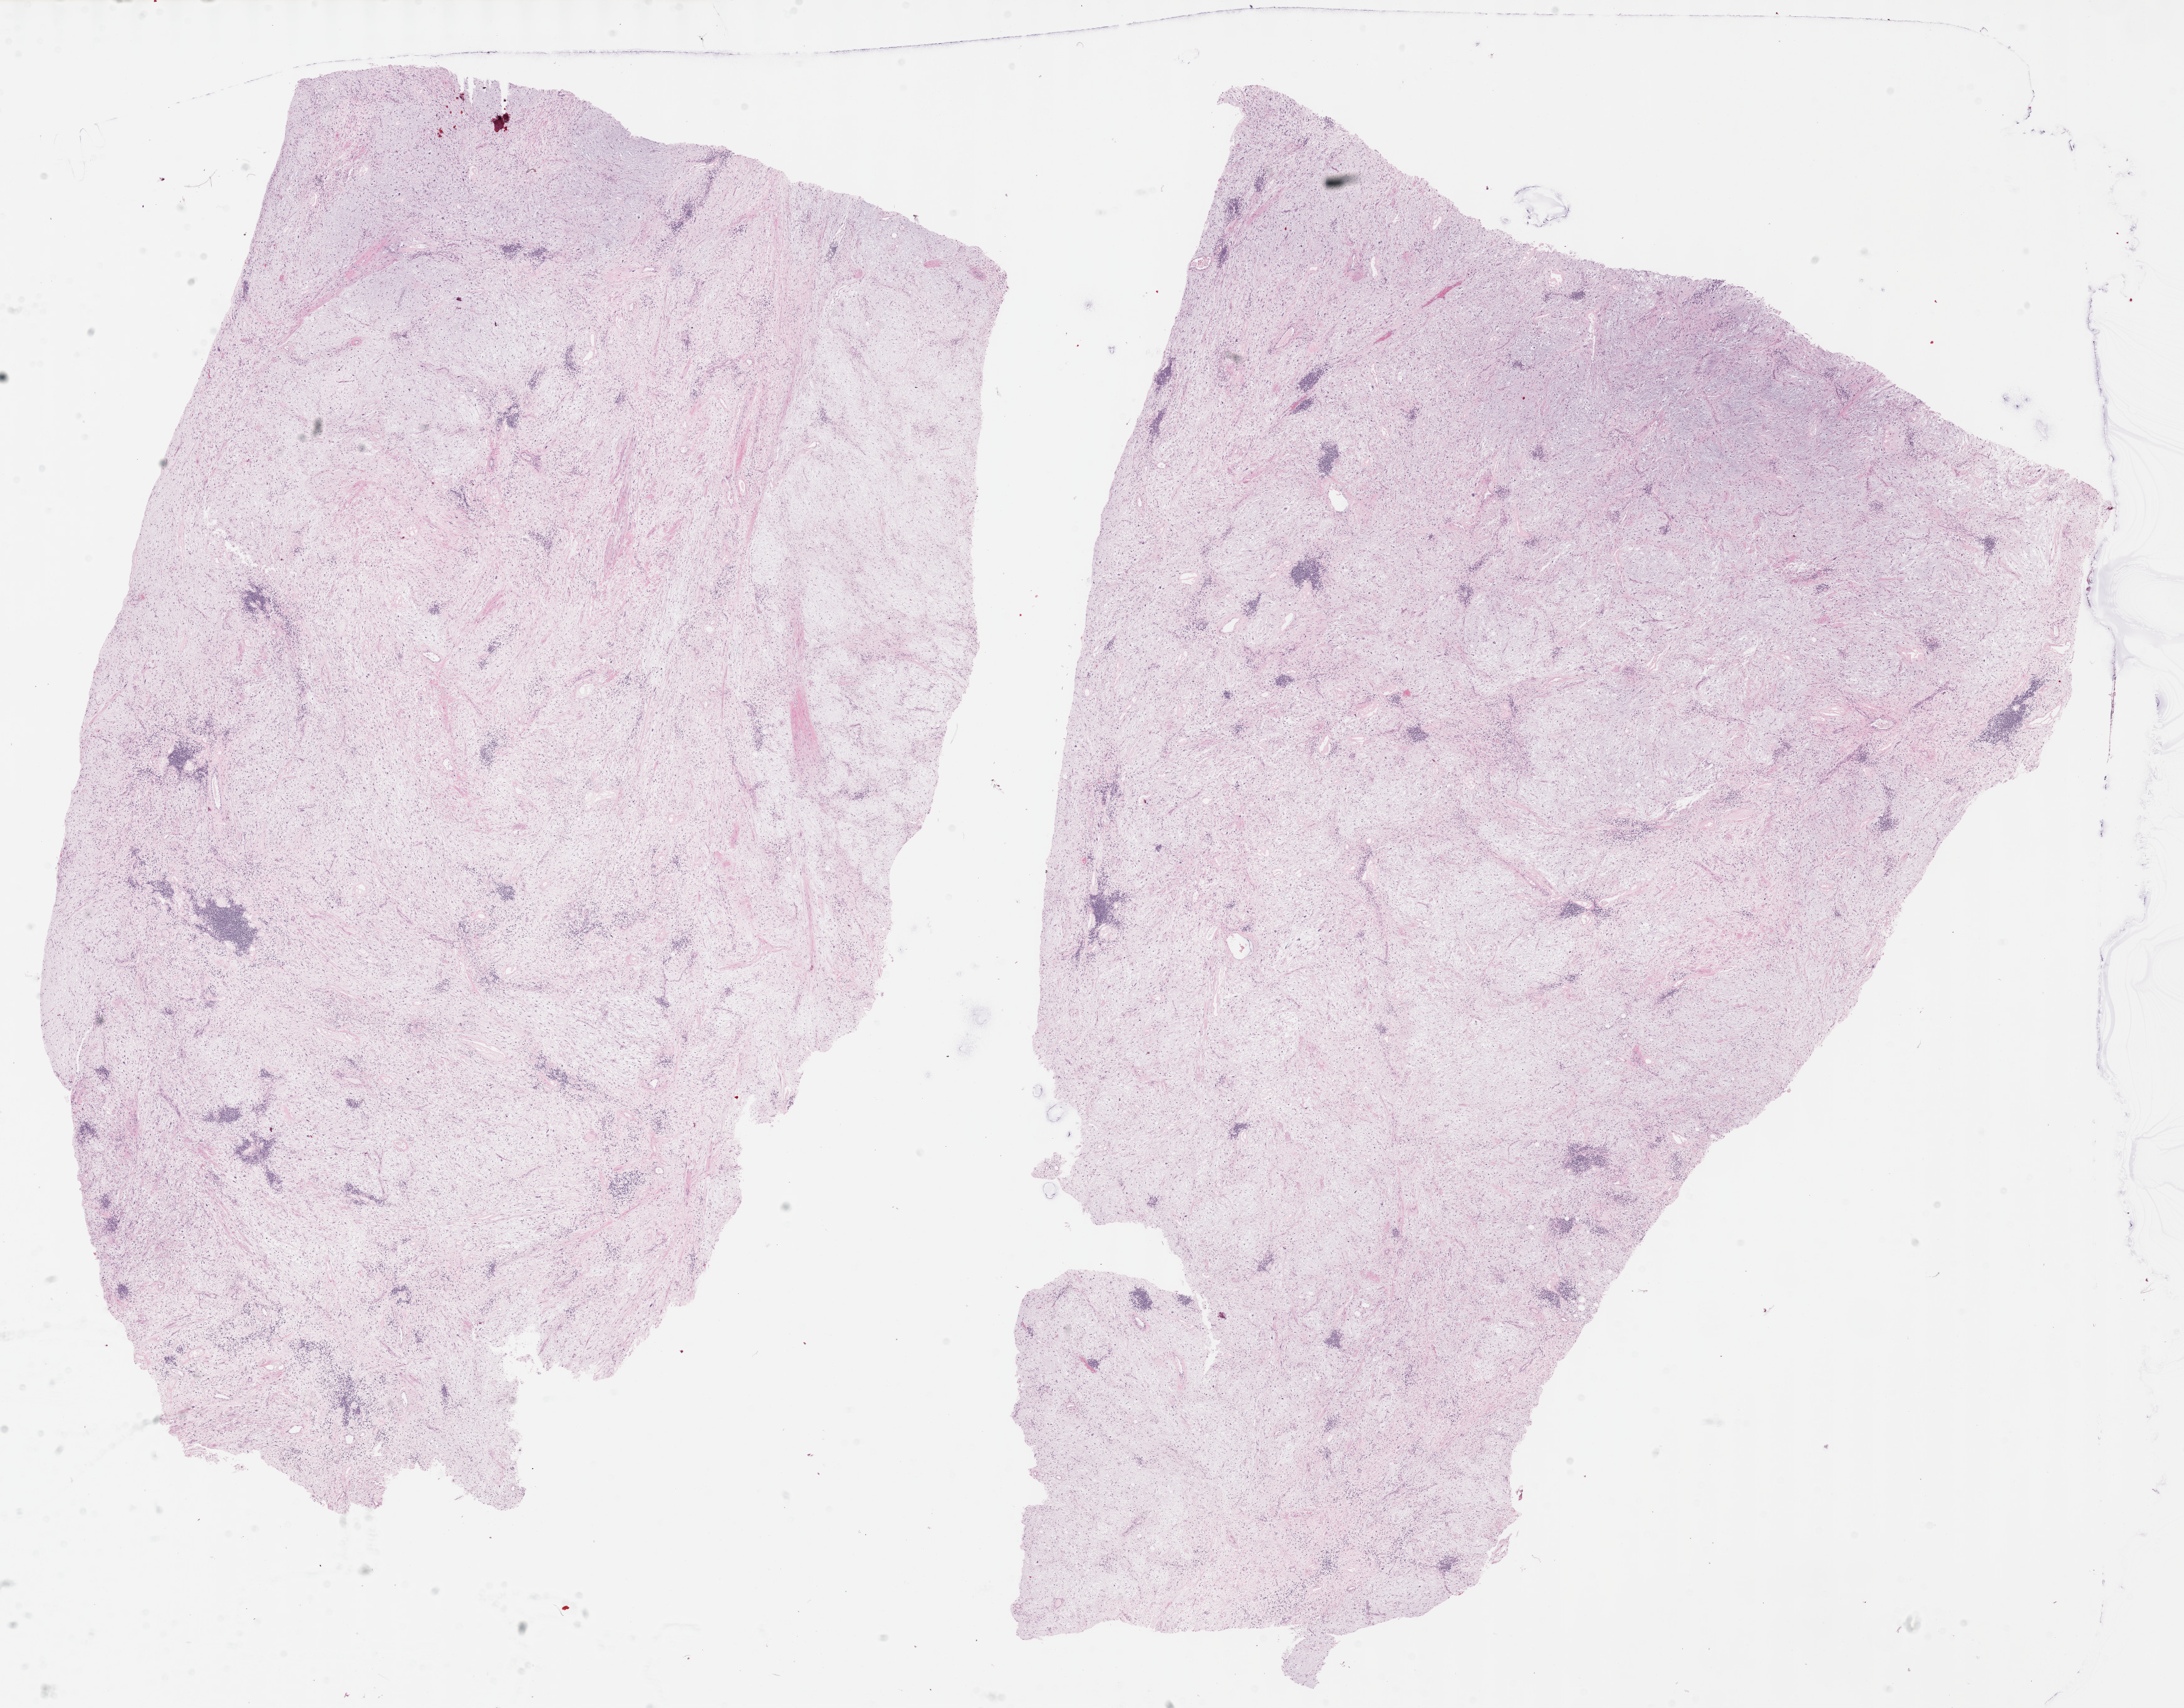
H&E-stained whole-slide image — shown as a low-resolution overview of the whole scanned area (about 28.2 x 22.0 mm, acquisition: 40x scan); formalin-fixed paraffin-embedded (FFPE) diagnostic section; sample: primary tumour, retroperitoneum and peritoneum. Female patient; age at initial diagnosis 50 years.
Diagnosis: Dedifferentiated liposarcoma (retroperitoneum).